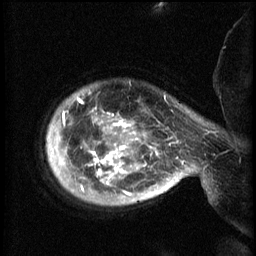
Breast MRI (dynamic contrast-enhanced), one sagittal slice; slice 52 of 60 in the series (ordered by position); 3 images stored at this slice position (order not interpretable as contrast timing); 1.5 T; TE 4.2 ms, TR 8.2 ms; 2.3 mm slice thickness; 256 × 256 image matrix. Female patient, age 50 years.
Annotated regions visible in this slice (semi-automatically segmented with operator editing):
- analysis volume of interest (the breast-tissue region the enhancement analysis was run in; not a lesion): bounding box (x1, y1, x2, y2) in pixels: (50, 88, 169, 205)
- tumour enhancement mask (voxels above the 70 % enhancement threshold inside the analysis volume of interest): (62, 98, 169, 195)